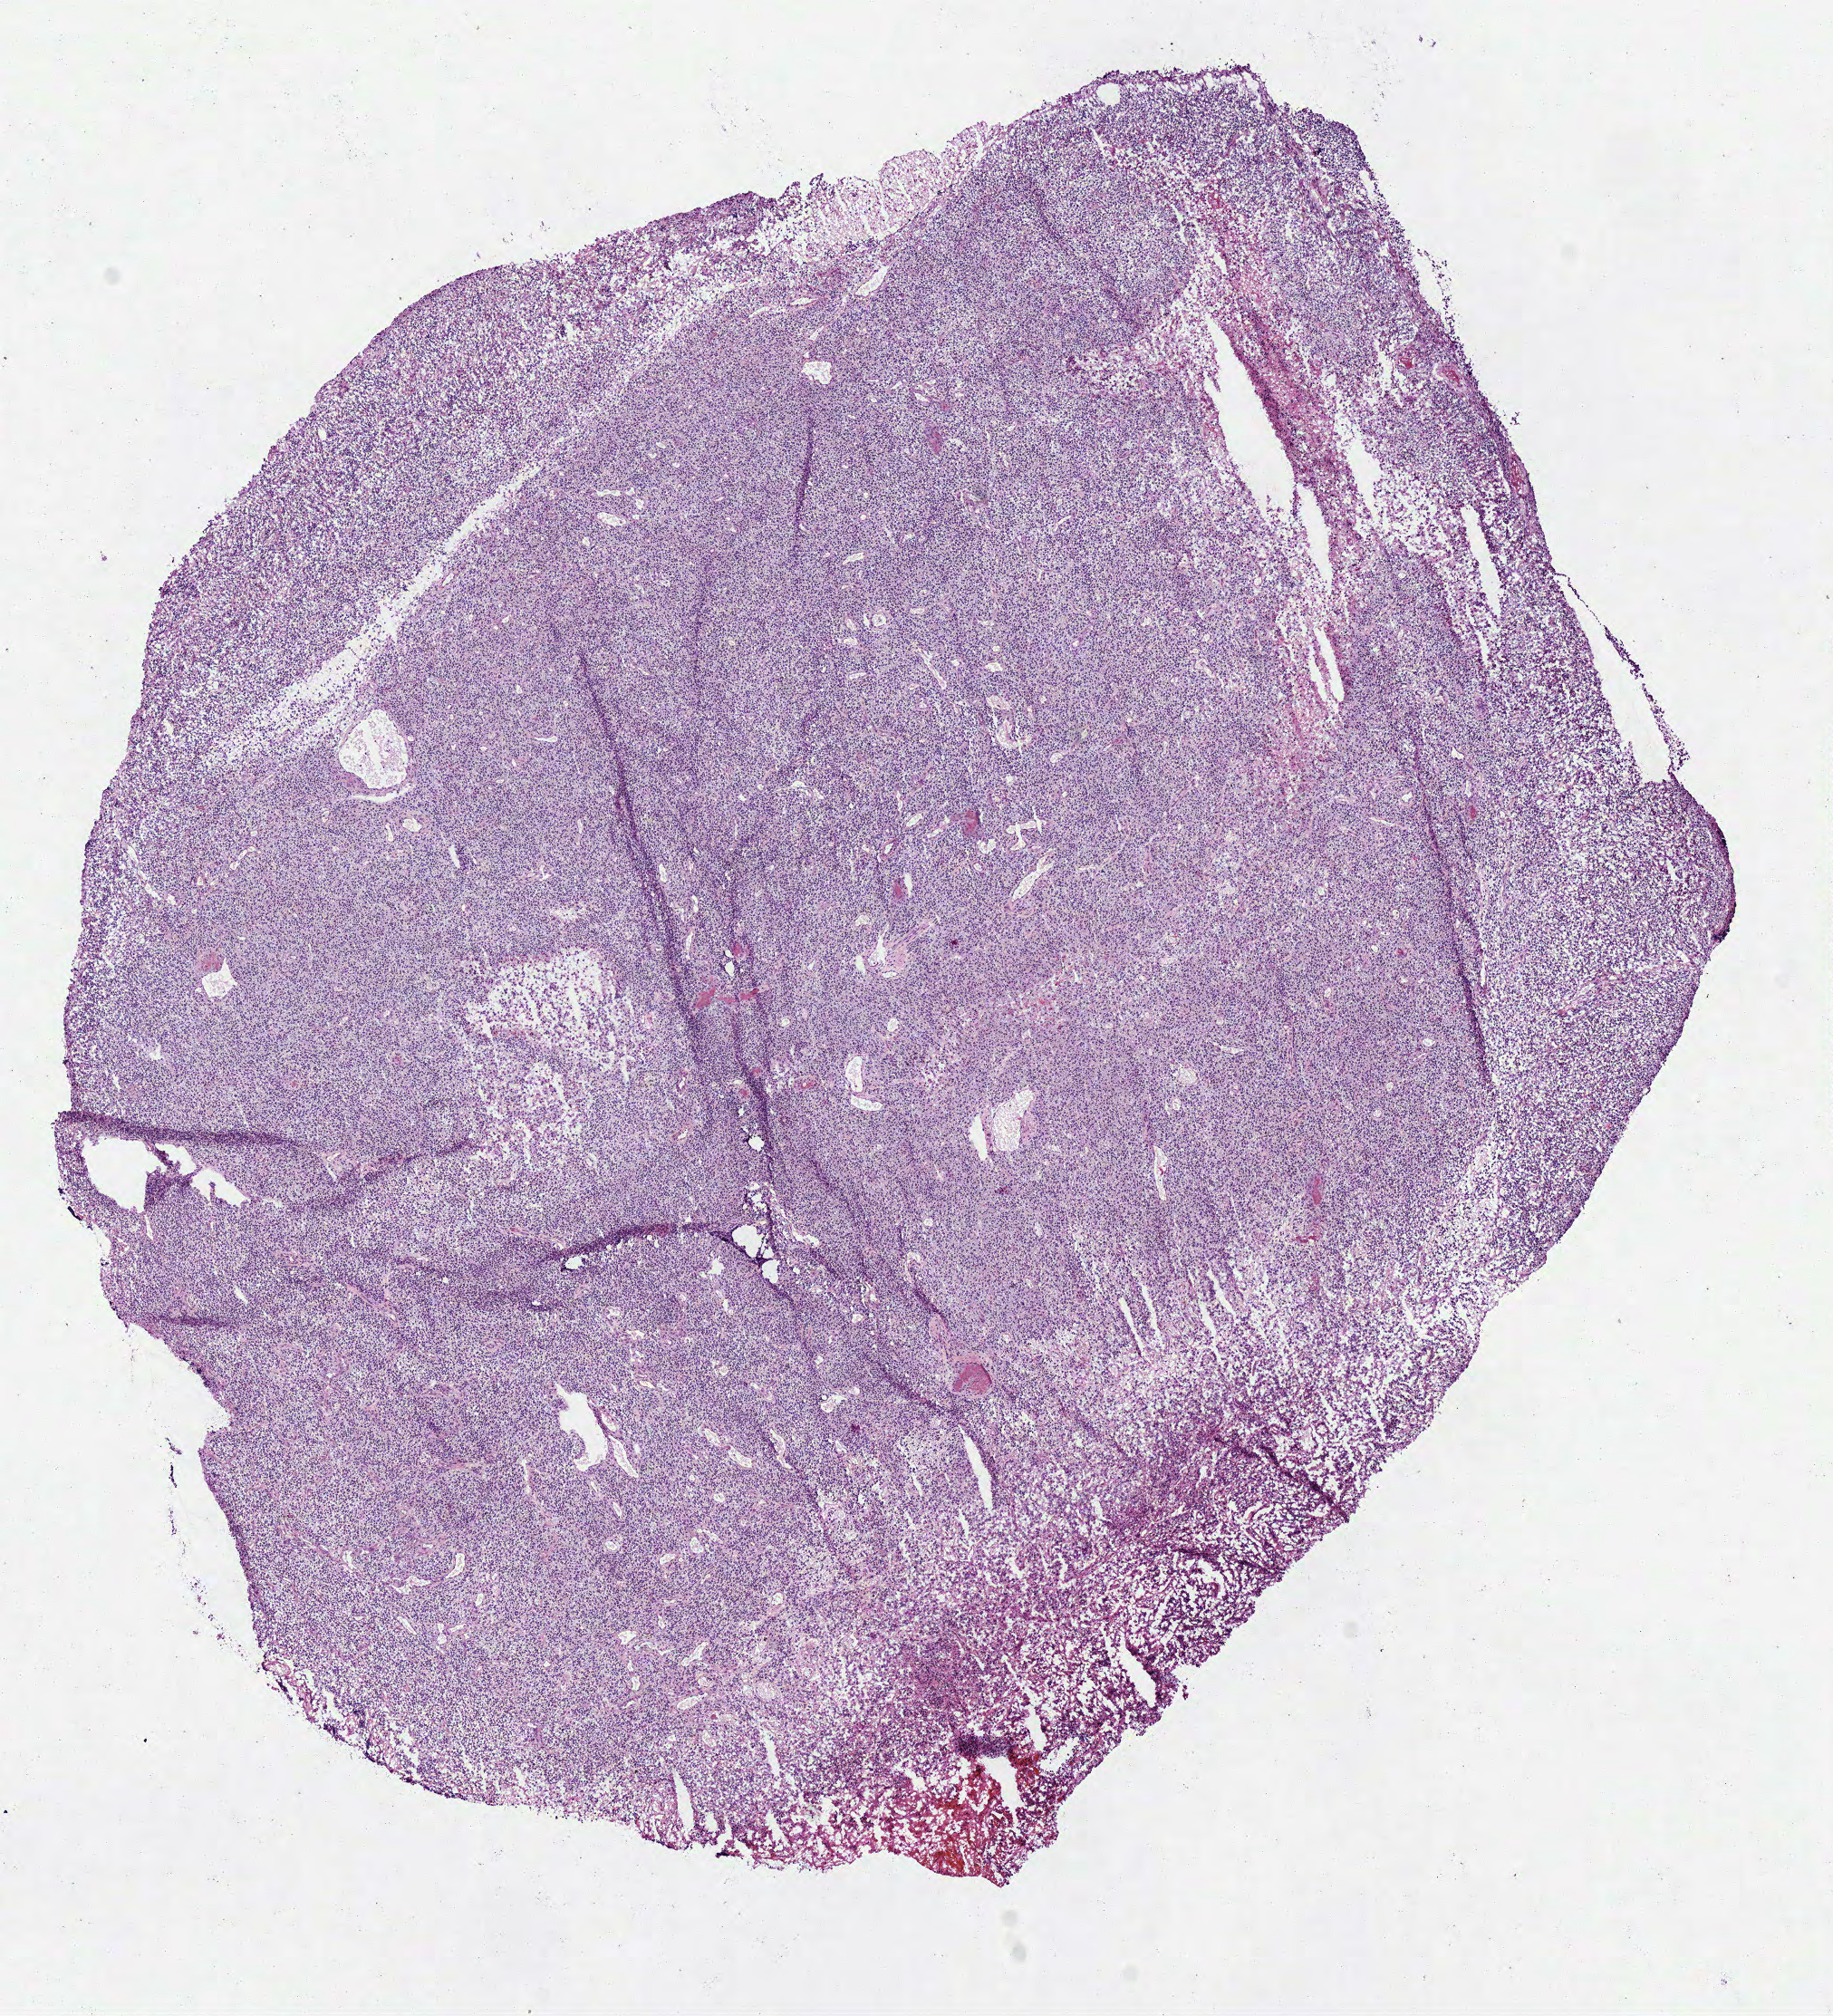
Whole-slide histology image, Hematoxylin and eosin (H&E) stained, a low-resolution overview of the entire scanned area, about 8.0 x 8.8 mm (slide scanned at 40x). Frozen section from the bottom of the tissue portion. Sample: primary tumour, brain. Male, age 52 years at initial diagnosis. Pathologist review of this section (percent, as recorded): tumour cells 85%, tumour nuclei 85%, normal cells 0%, stromal cells 0%, necrosis 15%.
- pathologic diagnosis: Glioblastoma